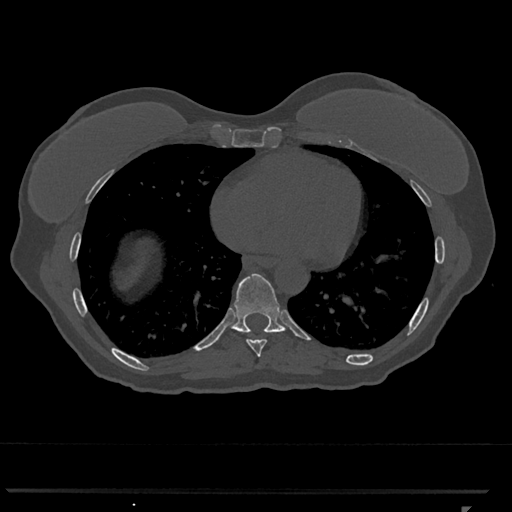
CT including the spine, one axial slice. Slice 639 of 793 in the series (ordered by position). Reconstruction kernel Br40s/3. Bone window (W 1800 / L 400 HU). 512 × 512 image matrix. Patient: female, 62 years. Case-level facts recorded for this patient, not image findings: primary cancer: renal.
Annotated regions visible in this slice (semi-automatically segmented with operator editing):
- T8 vertebra: bounding box <246,339,267,357> (left, top, right, bottom; pixels)
- T9 vertebra: <231,273,286,333>